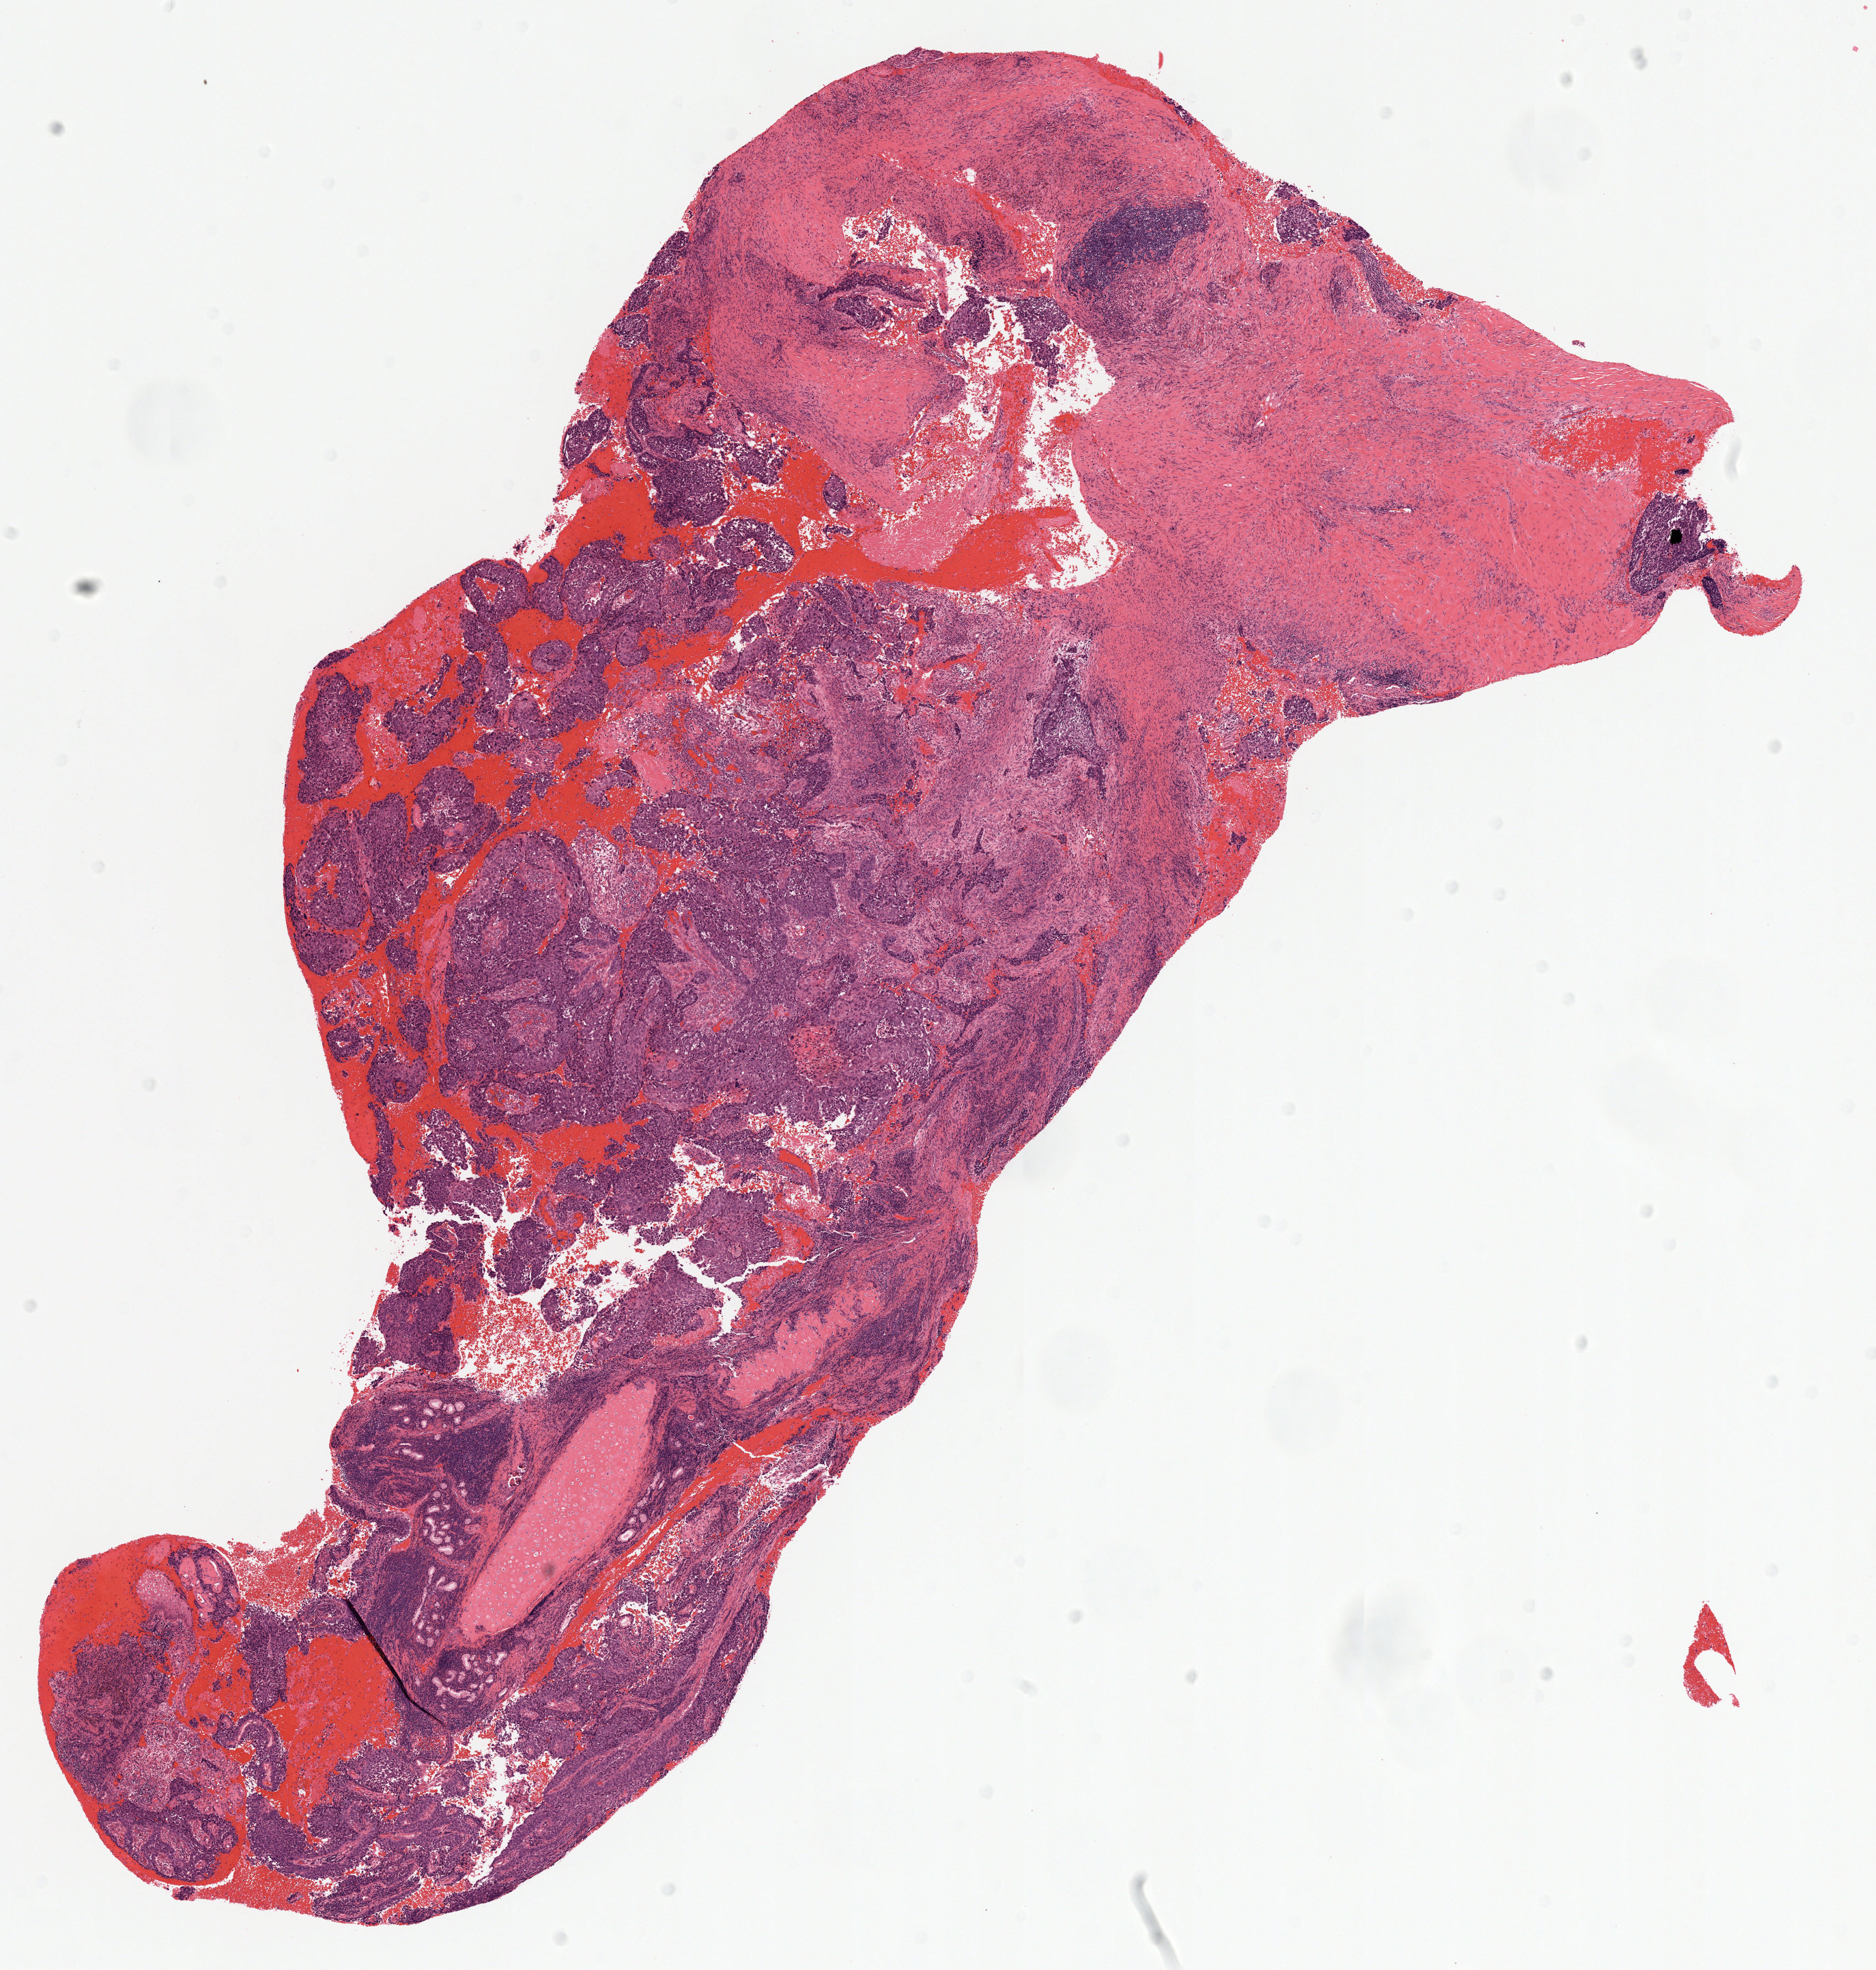
Digitized H&E tissue section (whole slide) — whole scanned area (about 11.0 x 11.6 mm, acquisition: 20x scan) shown as a low-resolution overview. Formalin-fixed paraffin-embedded (FFPE) diagnostic section. Primary tumour sample from the lung. Male patient; age at initial diagnosis 54 years.
AJCC pathologic stage: IIB (6th edition). Histologic diagnosis: Squamous cell carcinoma, NOS.